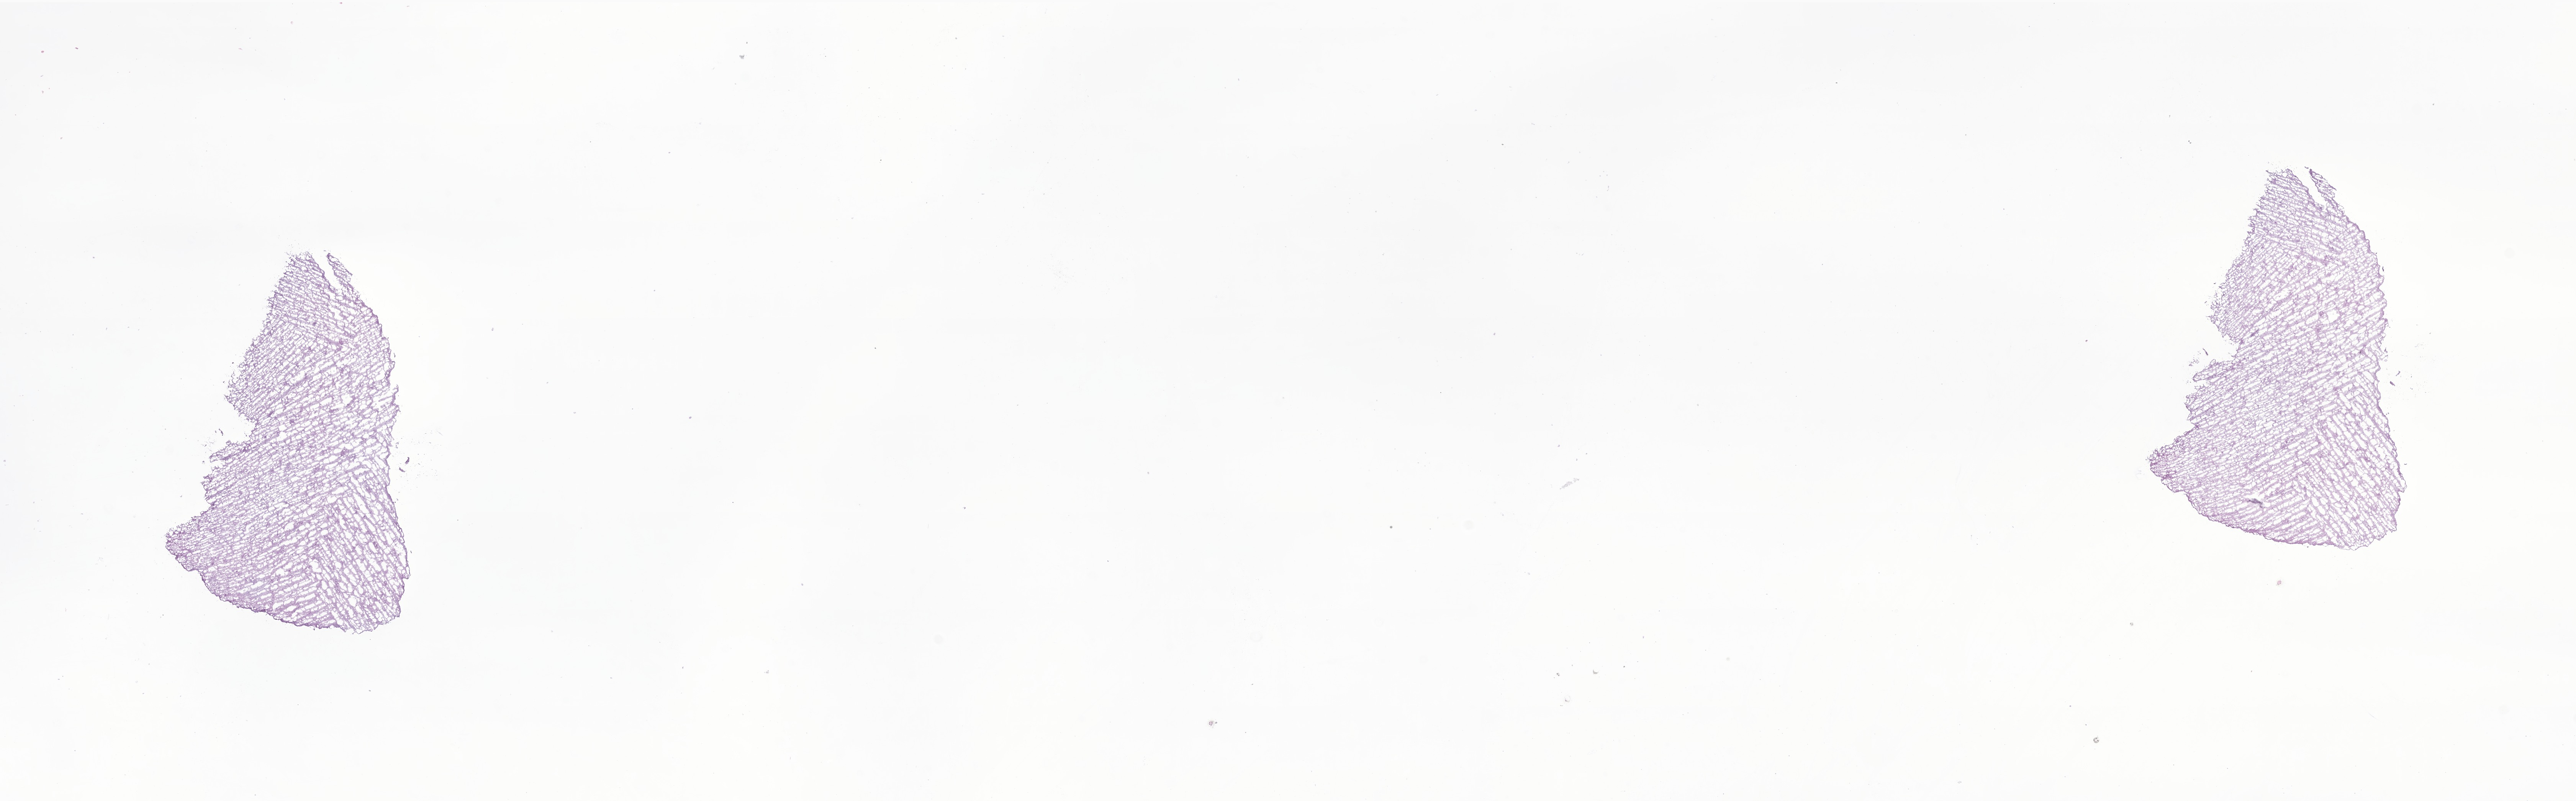
Digitized H&E-stained section of tumor tissue from the cerebellum — whole scanned area (about 28.4 x 8.8 mm) shown as a low-resolution overview; cryosection (OCT / tissue freezing medium). Patient: female, age 196 months (16 years 4 months).
Recorded diagnosis: Pilocytic astrocytoma.